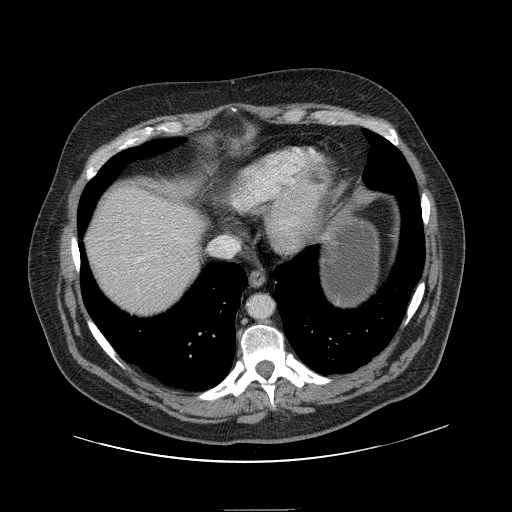
Contrast-enhanced abdominal CT, one axial slice. Position 133 of 154 along the scan axis. 120 kVp. Soft-tissue window (W 400 / L 40 HU). 2.5 mm slice thickness. 512 × 512 image matrix, field of view 451 × 451 mm. Male patient, age 61 years. From the clinical record (not read from this slice): diagnosis: colorectal cancer liver metastases, imaged before liver resection; multiple liver metastases: yes; largest metastasis: 2.6 cm; disease in both lobes: yes.
Annotated regions visible in this slice (manually delineated by an expert):
- liver: box from (x=88, y=189) to (x=202, y=314) px
- planned liver remnant (the part of the liver to remain after resection): (x=88, y=188)–(x=200, y=314)
- portal vein (with intrahepatic branches): (x=128, y=216)–(x=143, y=262)